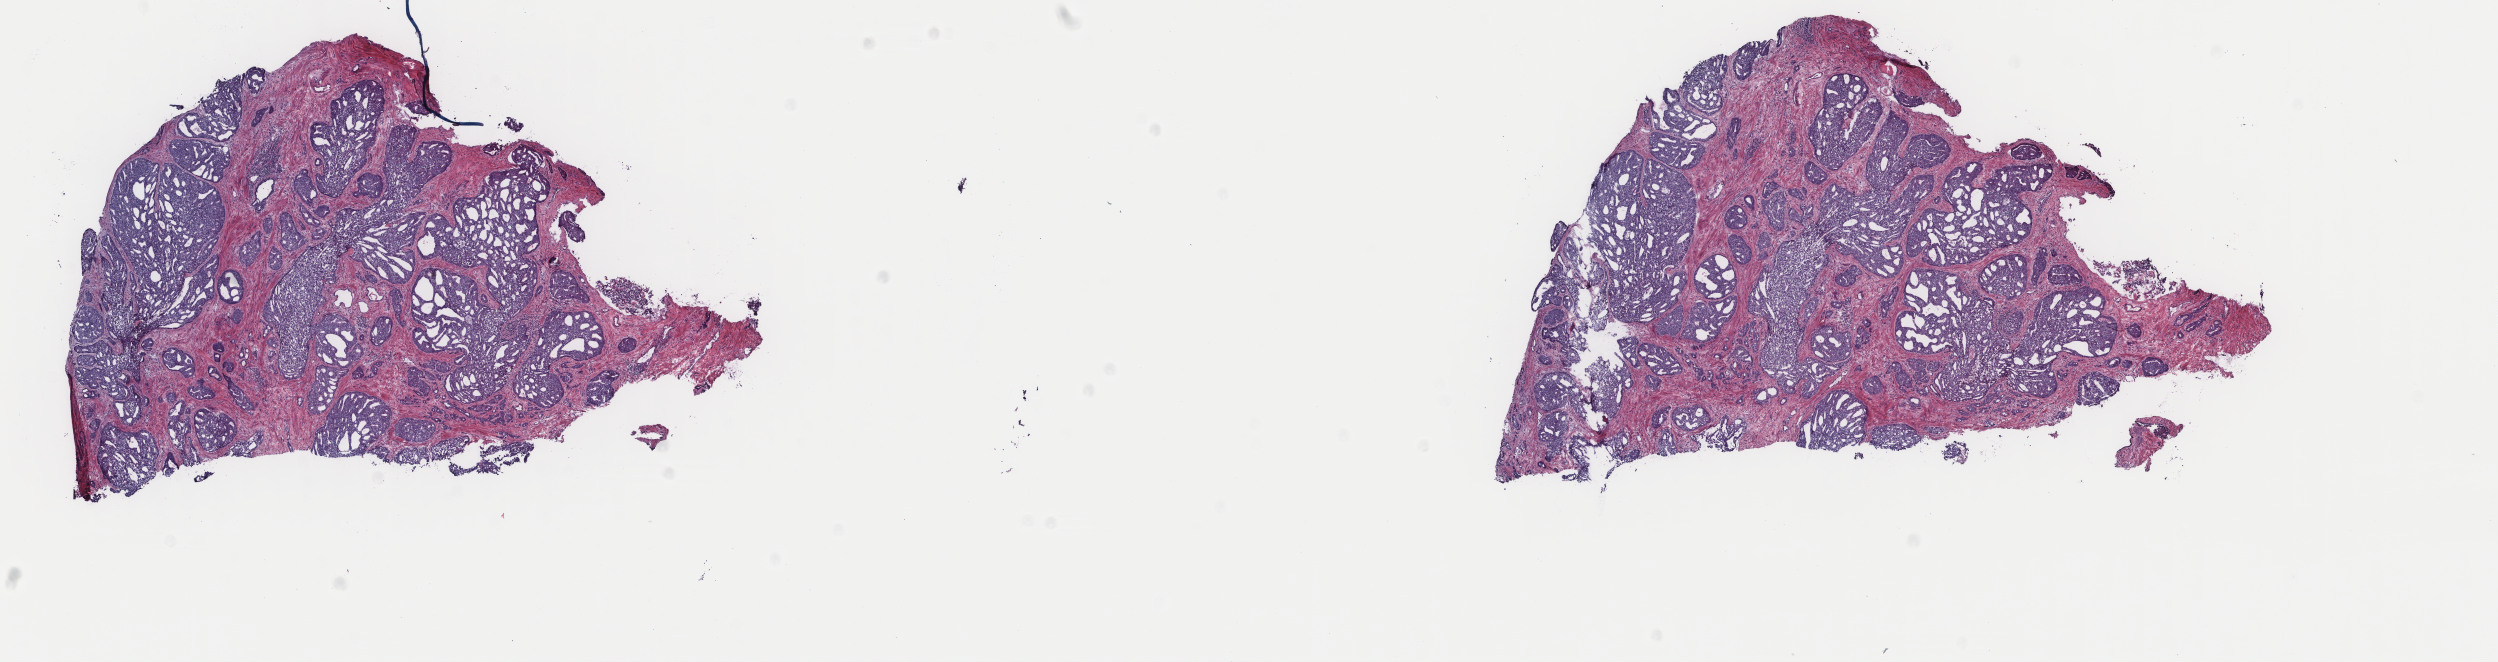
Whole-slide histology image, H&E — shown as a low-resolution overview of the whole scanned area (about 19.8 x 5.3 mm, from a 40x scan); frozen section from the top of the tissue portion; sample: primary tumour, prostate. Male patient; age at initial diagnosis 57 years.
Pathologic diagnosis: Adenocarcinoma, NOS.